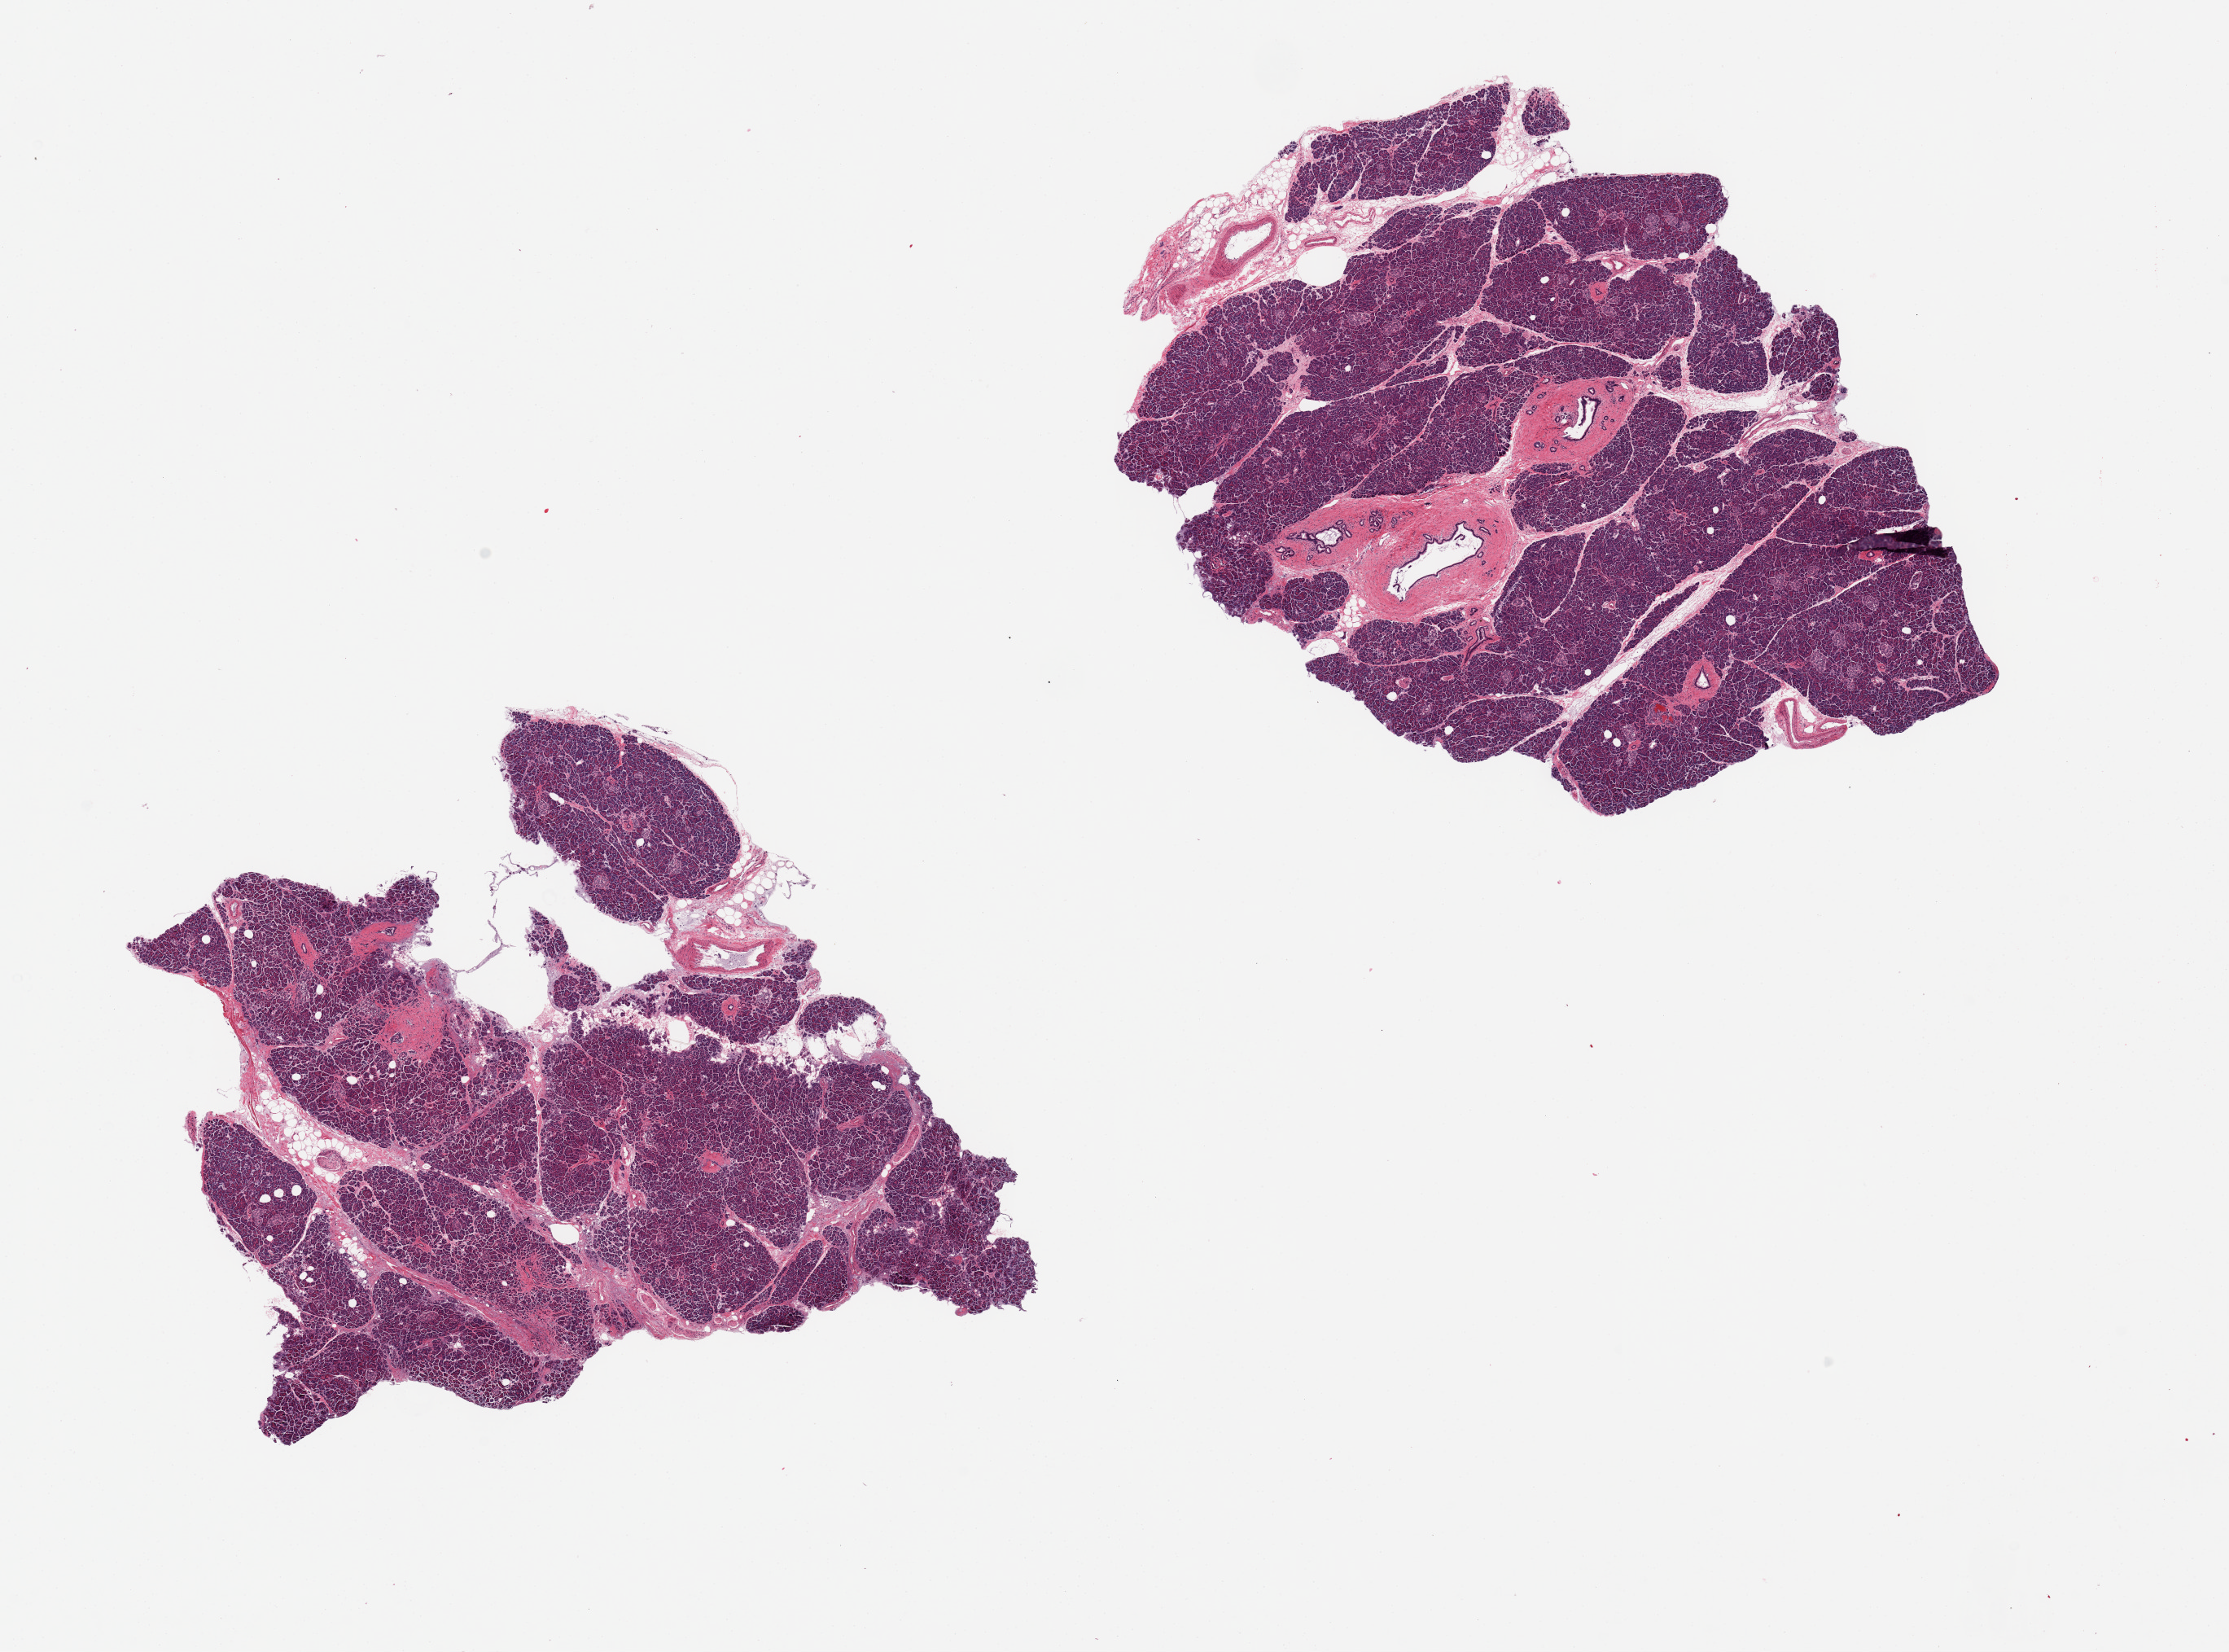
Digitized hematoxylin and eosin (H&E)-stained section — a low-resolution overview of the entire scanned area, about 21.7 x 16.0 mm (acquisition: 20x scan); PAXgene-fixed, paraffin-embedded tissue; sampled site (target tissue): pancreas; donor tissue sample. Donor sex: male.
Pathologist's review note for this sample: 2 pieces.